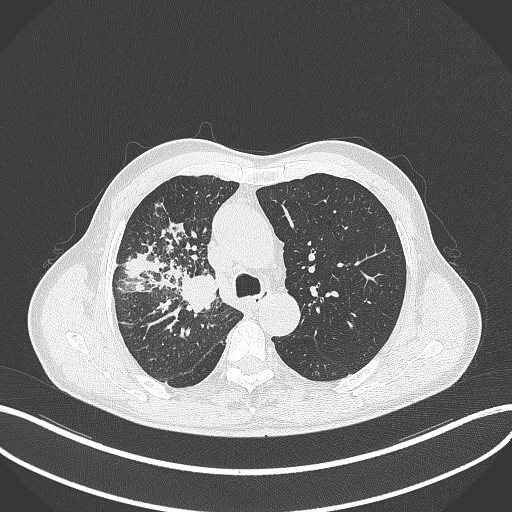
Chest CT, one axial slice; position 336 of 490 along the scan axis; lung window (W 1500 / L -600 HU); 512 × 512 image matrix. Male patient, age 69 years. From the clinical record (not read from this slice): clinical TNM (as recorded): T2a N0 M0.
Outlined on this slice (rectangle marked by the reading radiologist):
- lung tumour (recorded histology: adenocarcinoma): bounding box [x1, y1, x2, y2] px = [176, 270, 220, 313]